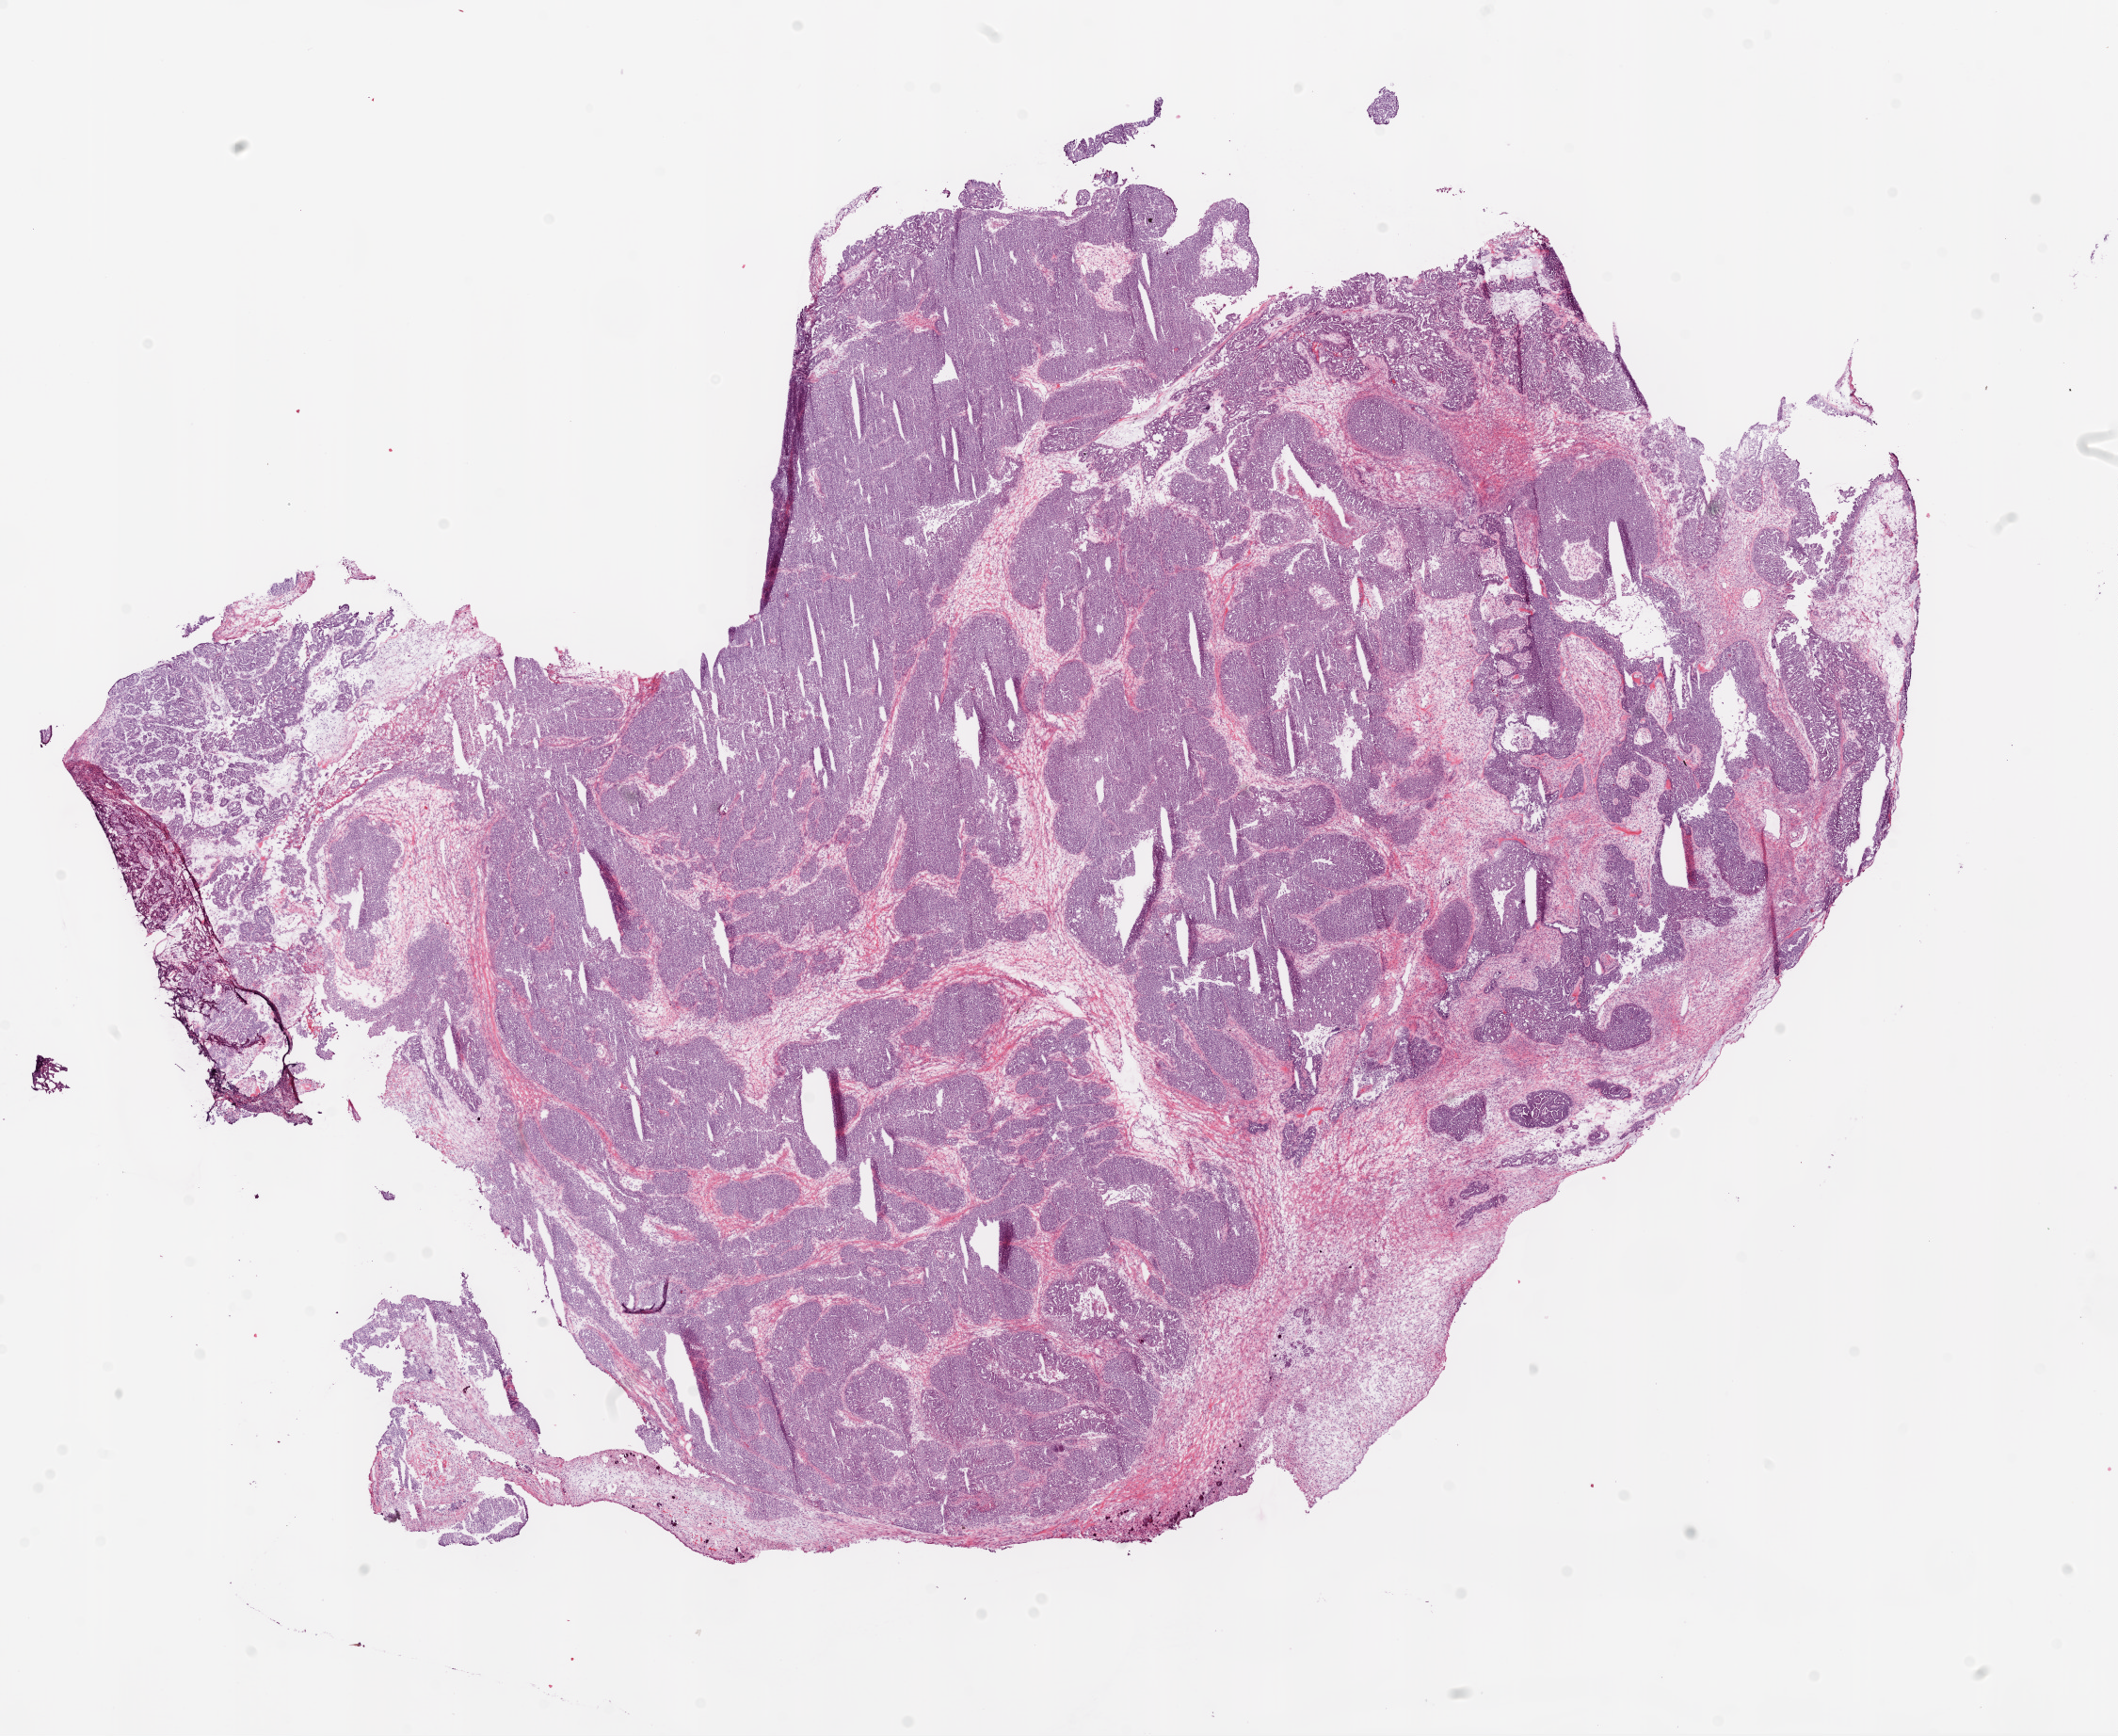
Whole-slide histology image, Hematoxylin and eosin (H&E) stained — low-resolution overview of the scanned area, about 18.1 x 14.8 mm, frozen section from the bottom of the tissue portion, ovary, primary tumour sample. Female patient; age at initial diagnosis 57 years. Histologic grade: G3 (poorly differentiated). Slide review estimates, as recorded: tumour cells 89%, tumour nuclei 90%, normal cells 1%, stromal cells 9%, necrosis 1%.
FIGO stage: IIIC. Diagnosis: Serous cystadenocarcinoma, NOS.